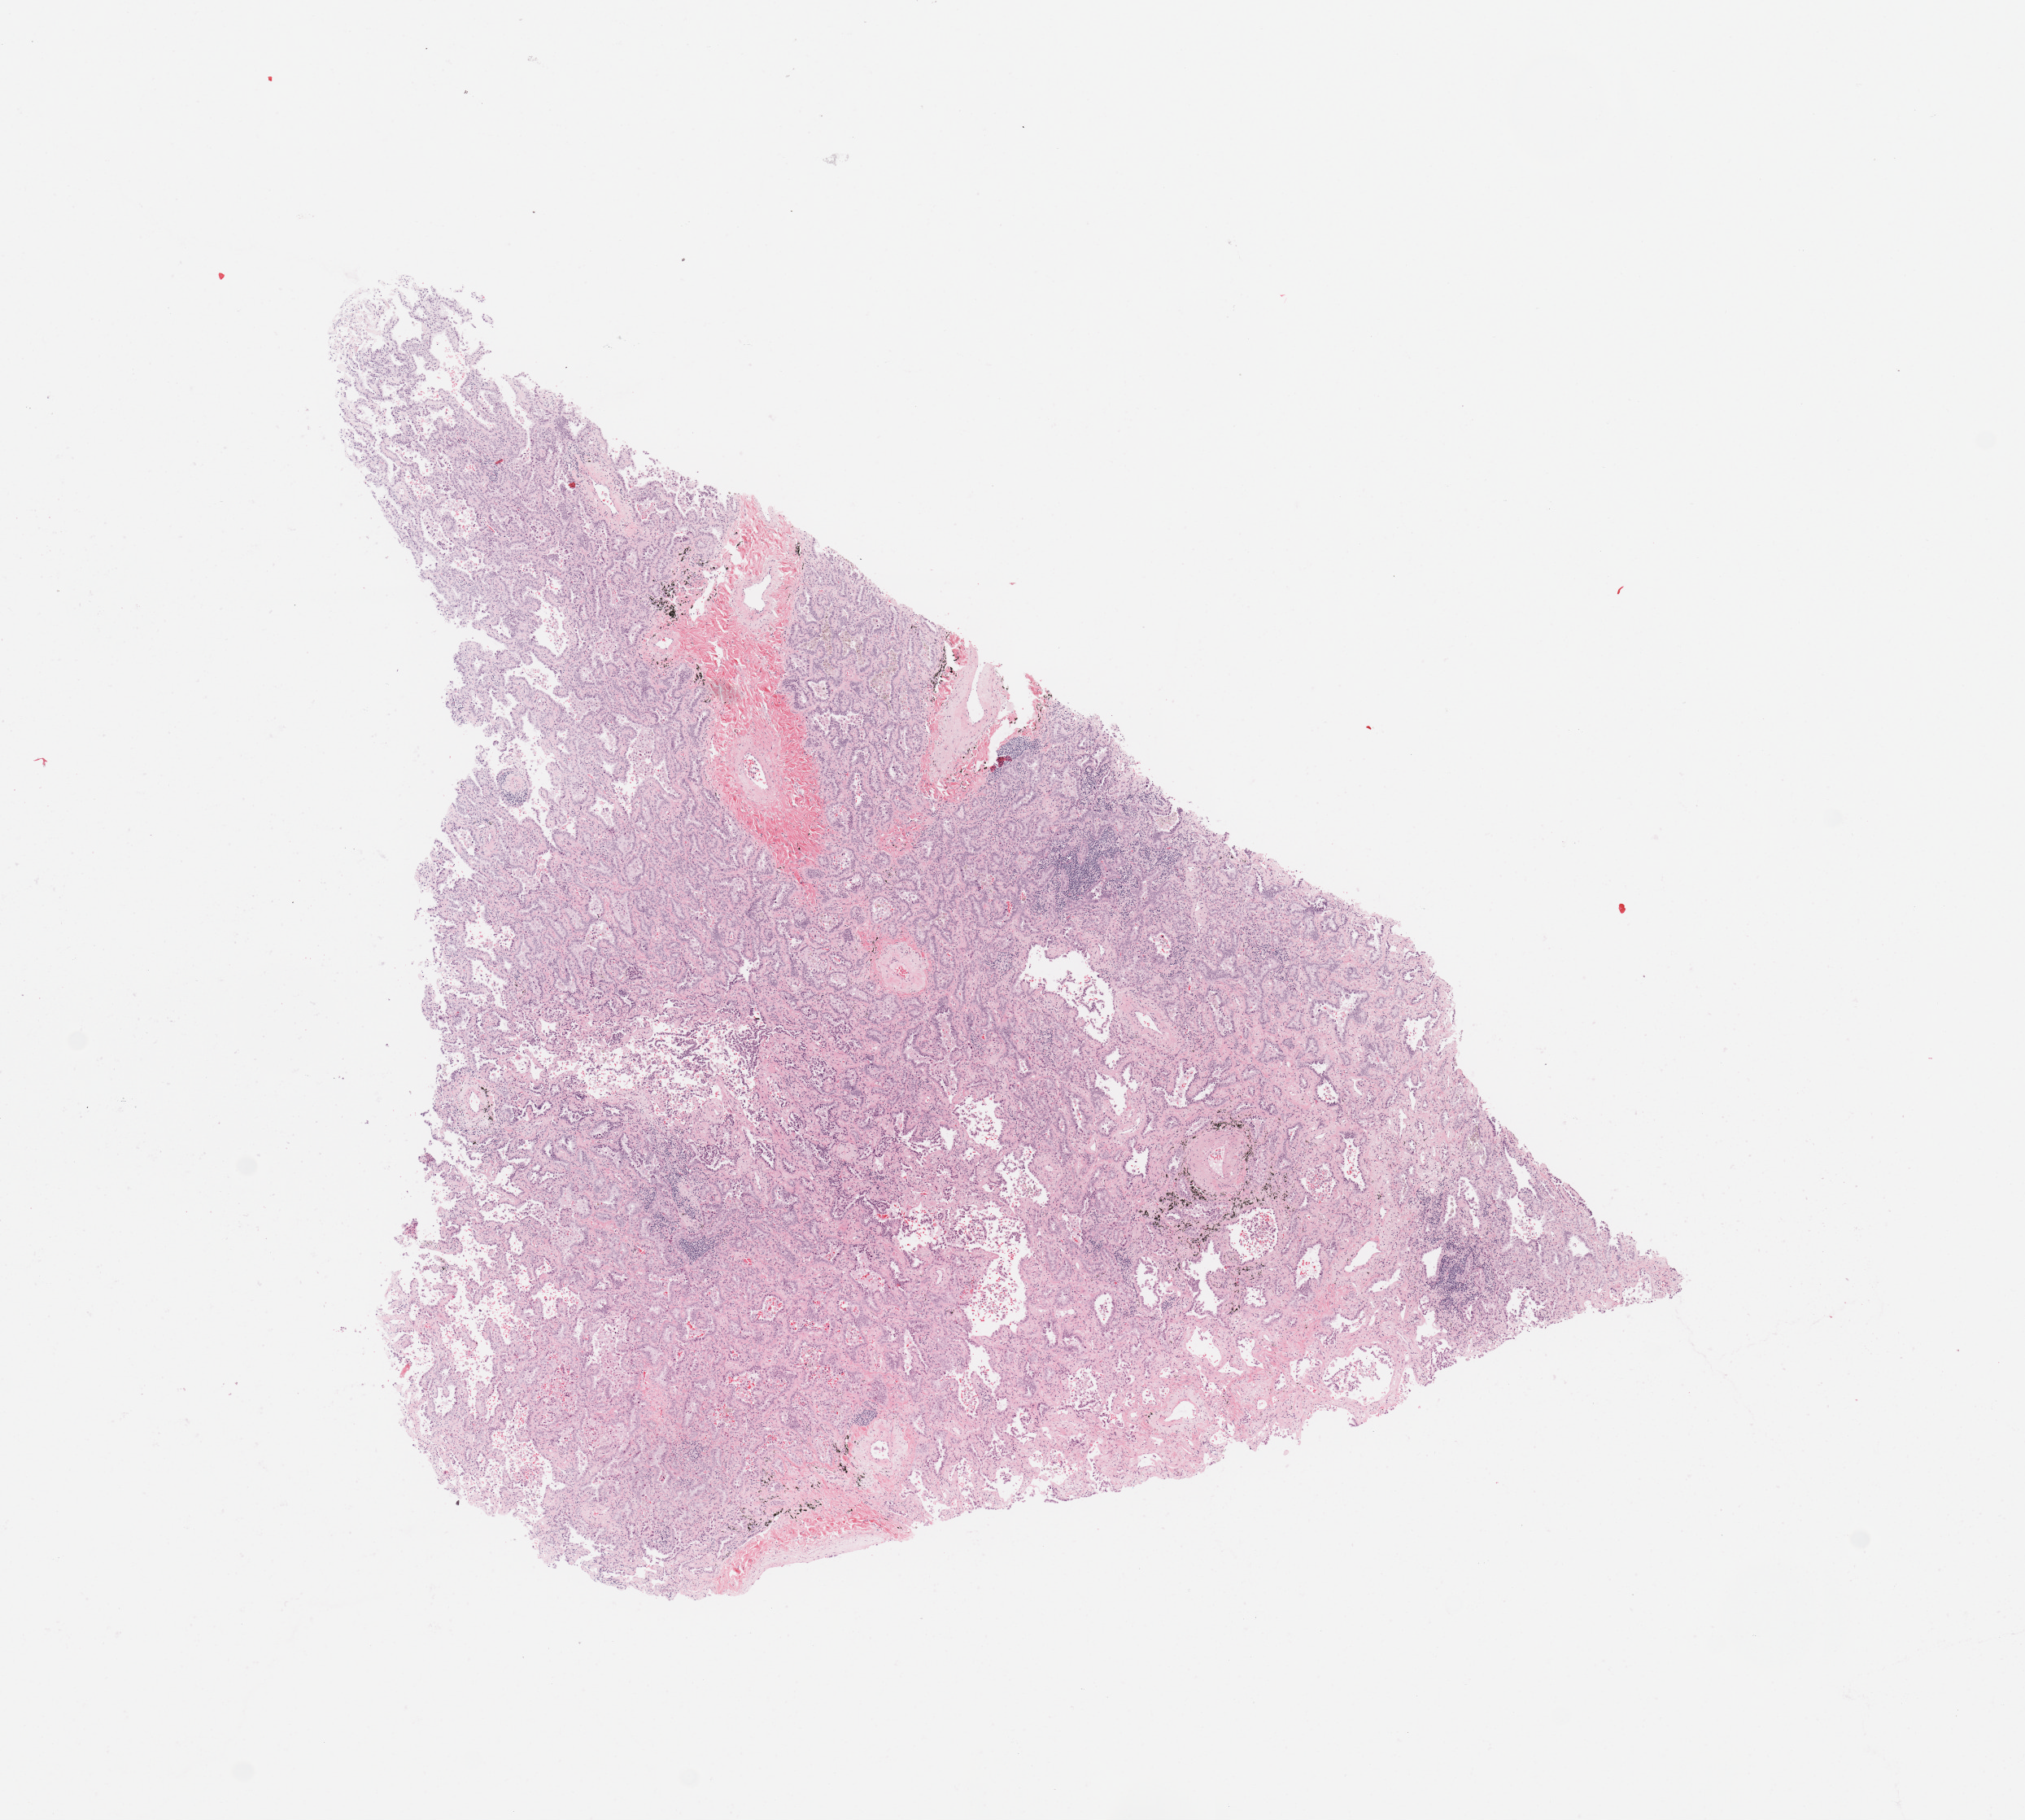
H&E-stained whole-slide image — low-resolution overview of the scanned area, about 9.8 x 8.8 mm (slide scanned at 20x); tumour tissue sample, sampled site: lung. Male, 58 y/o.
Diagnosis: Adenocarcinoma, NOS.